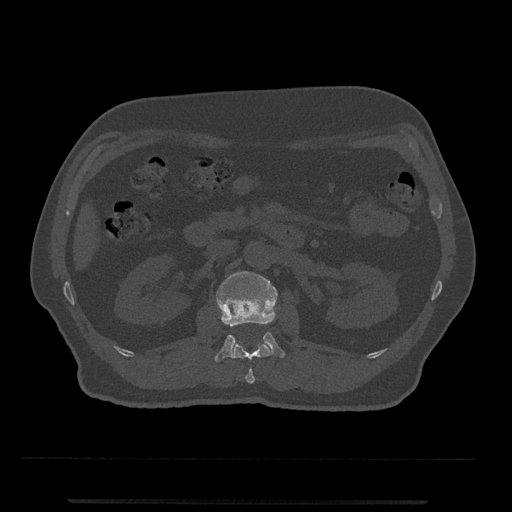
CT including the spine, one axial slice; slice 296 of 797 in the series (ordered by position); bone window (W 1800 / L 400 HU); 0.5 mm slice thickness; 512 × 512 image matrix. Patient: male, 63 years. Case-level facts recorded for this patient, not image findings: primary cancer: prostate.
Annotated regions visible in this slice (semi-automatically segmented with operator editing):
- L1 vertebra: bounding box [x1, y1, x2, y2] px = [231, 342, 273, 384]
- L2 vertebra: [214, 271, 285, 362]